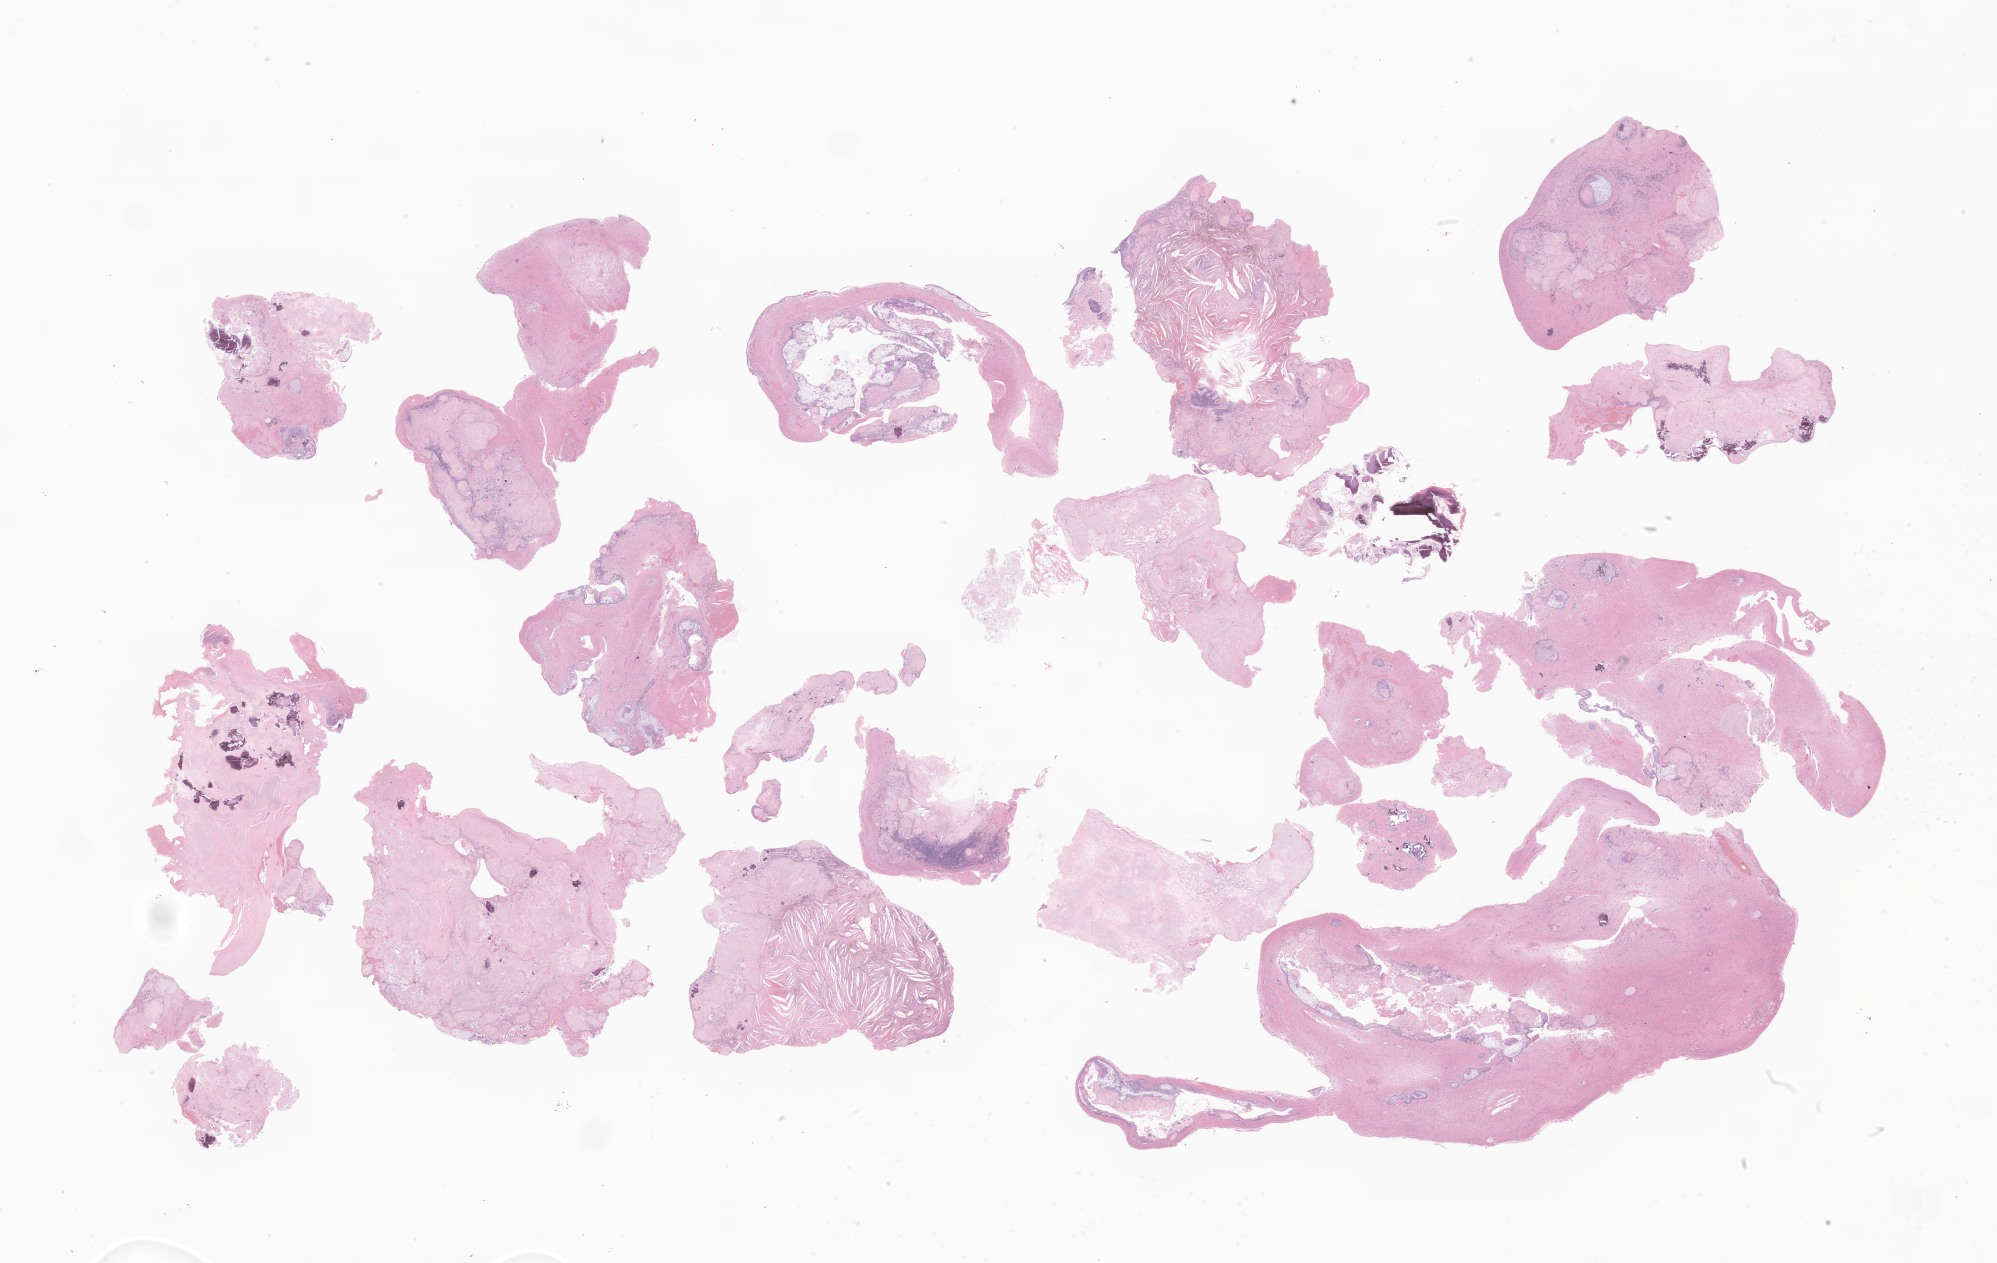
Digitized hematoxylin and eosin (H&E)-stained section of tumor tissue from the brain, low-resolution overview of the scanned area, about 33.7 x 21.3 mm; formalin-fixed, paraffin-embedded (FFPE) tissue. Patient: female, age 162 months (13 years 6 months).
Recorded diagnosis: Craniopharyngioma, adamantinomatous.